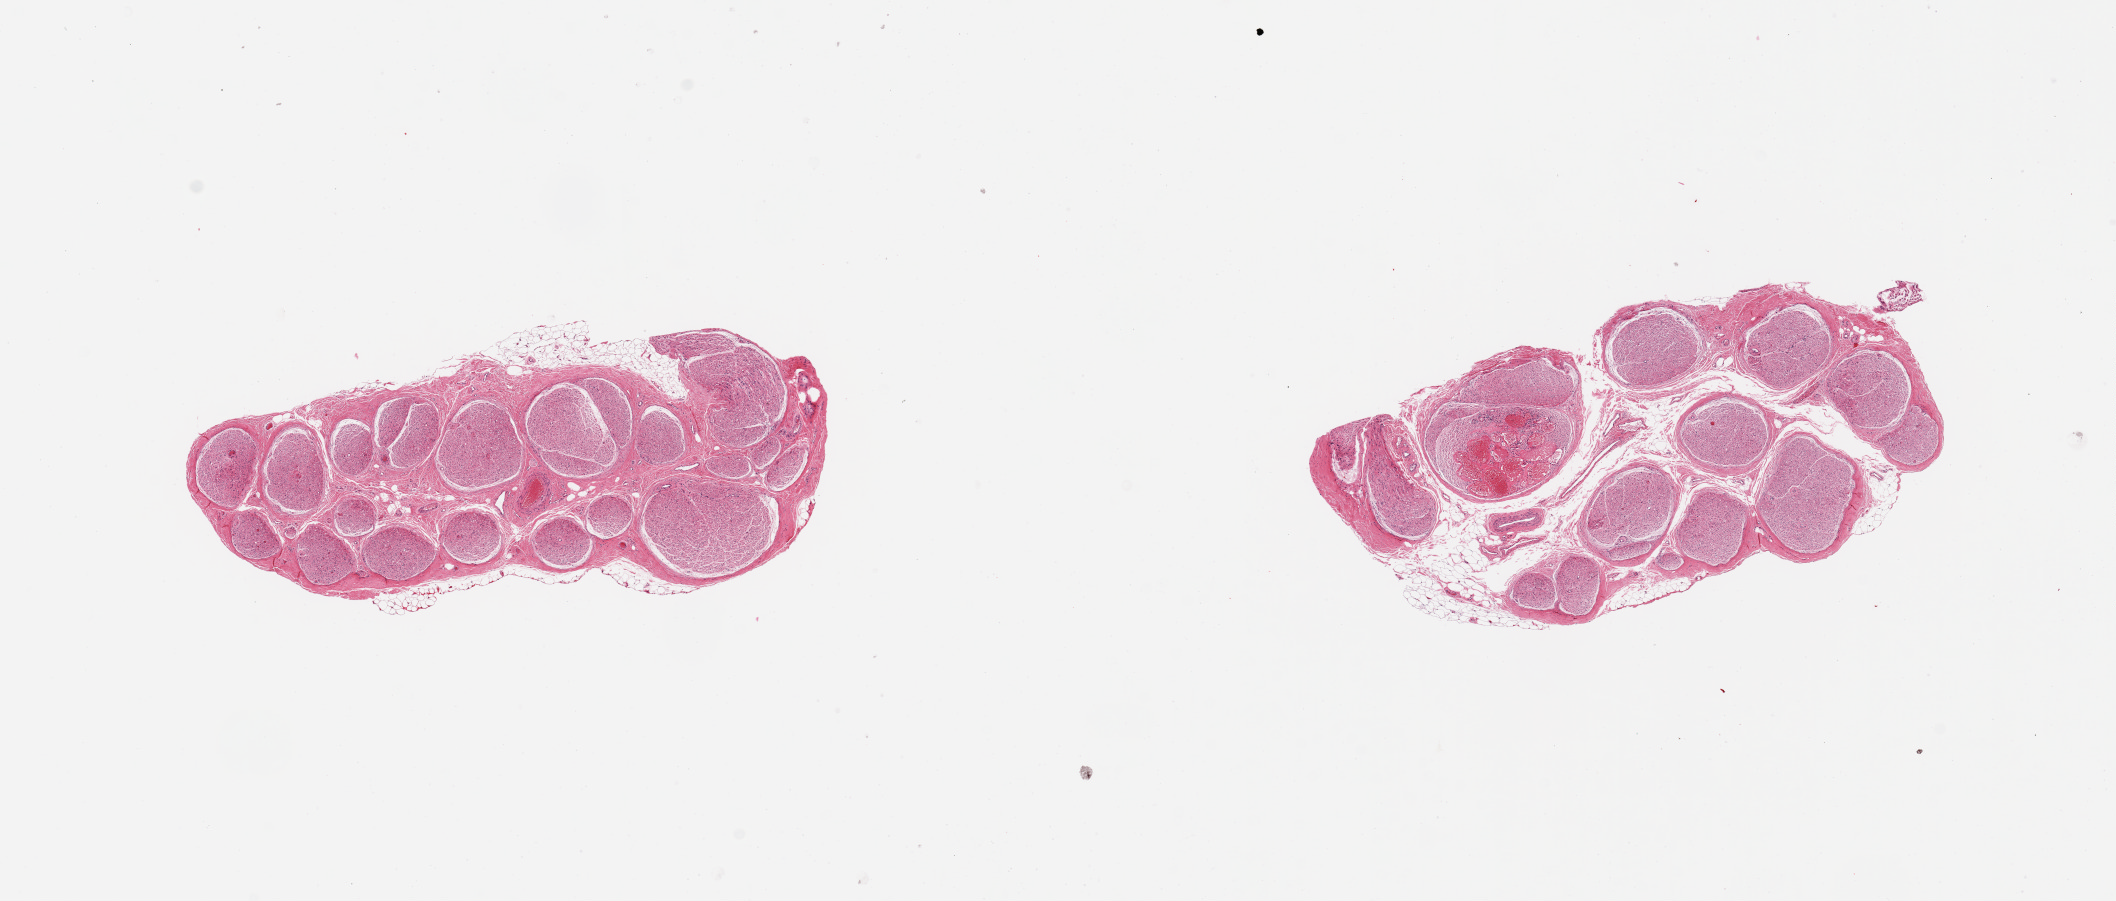
Hematoxylin and eosin (H&E) whole-slide image, whole scanned area (about 16.7 x 7.1 mm) shown as a low-resolution overview, PAXgene-fixed paraffin-embedded (PFPE) section, sampled site (target tissue): tibial nerve, donor tissue sample. Donor: female.
Review note (as recorded): 2 pieces, good specimen, trace adherent fat.